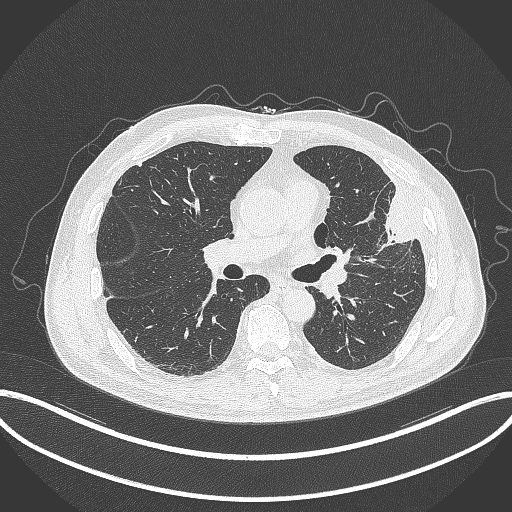
Chest CT, one axial slice. Slice 184 of 382 in the series (ordered by position). Reconstruction kernel B70f. 120 kVp. Lung window (W 1500 / L -600 HU). 1 mm slice thickness. 512 × 512 image matrix, field of view 415 × 415 mm. Patient: male, 64 years. Case-level facts recorded for this patient, not image findings: clinical TNM (as recorded): T4 N1 M0; histopathological grade: G3.
Annotated regions visible in this slice (rectangle marked by the reading radiologist):
- lung tumour (recorded histology: adenocarcinoma): box from (x=373, y=190) to (x=423, y=250) px